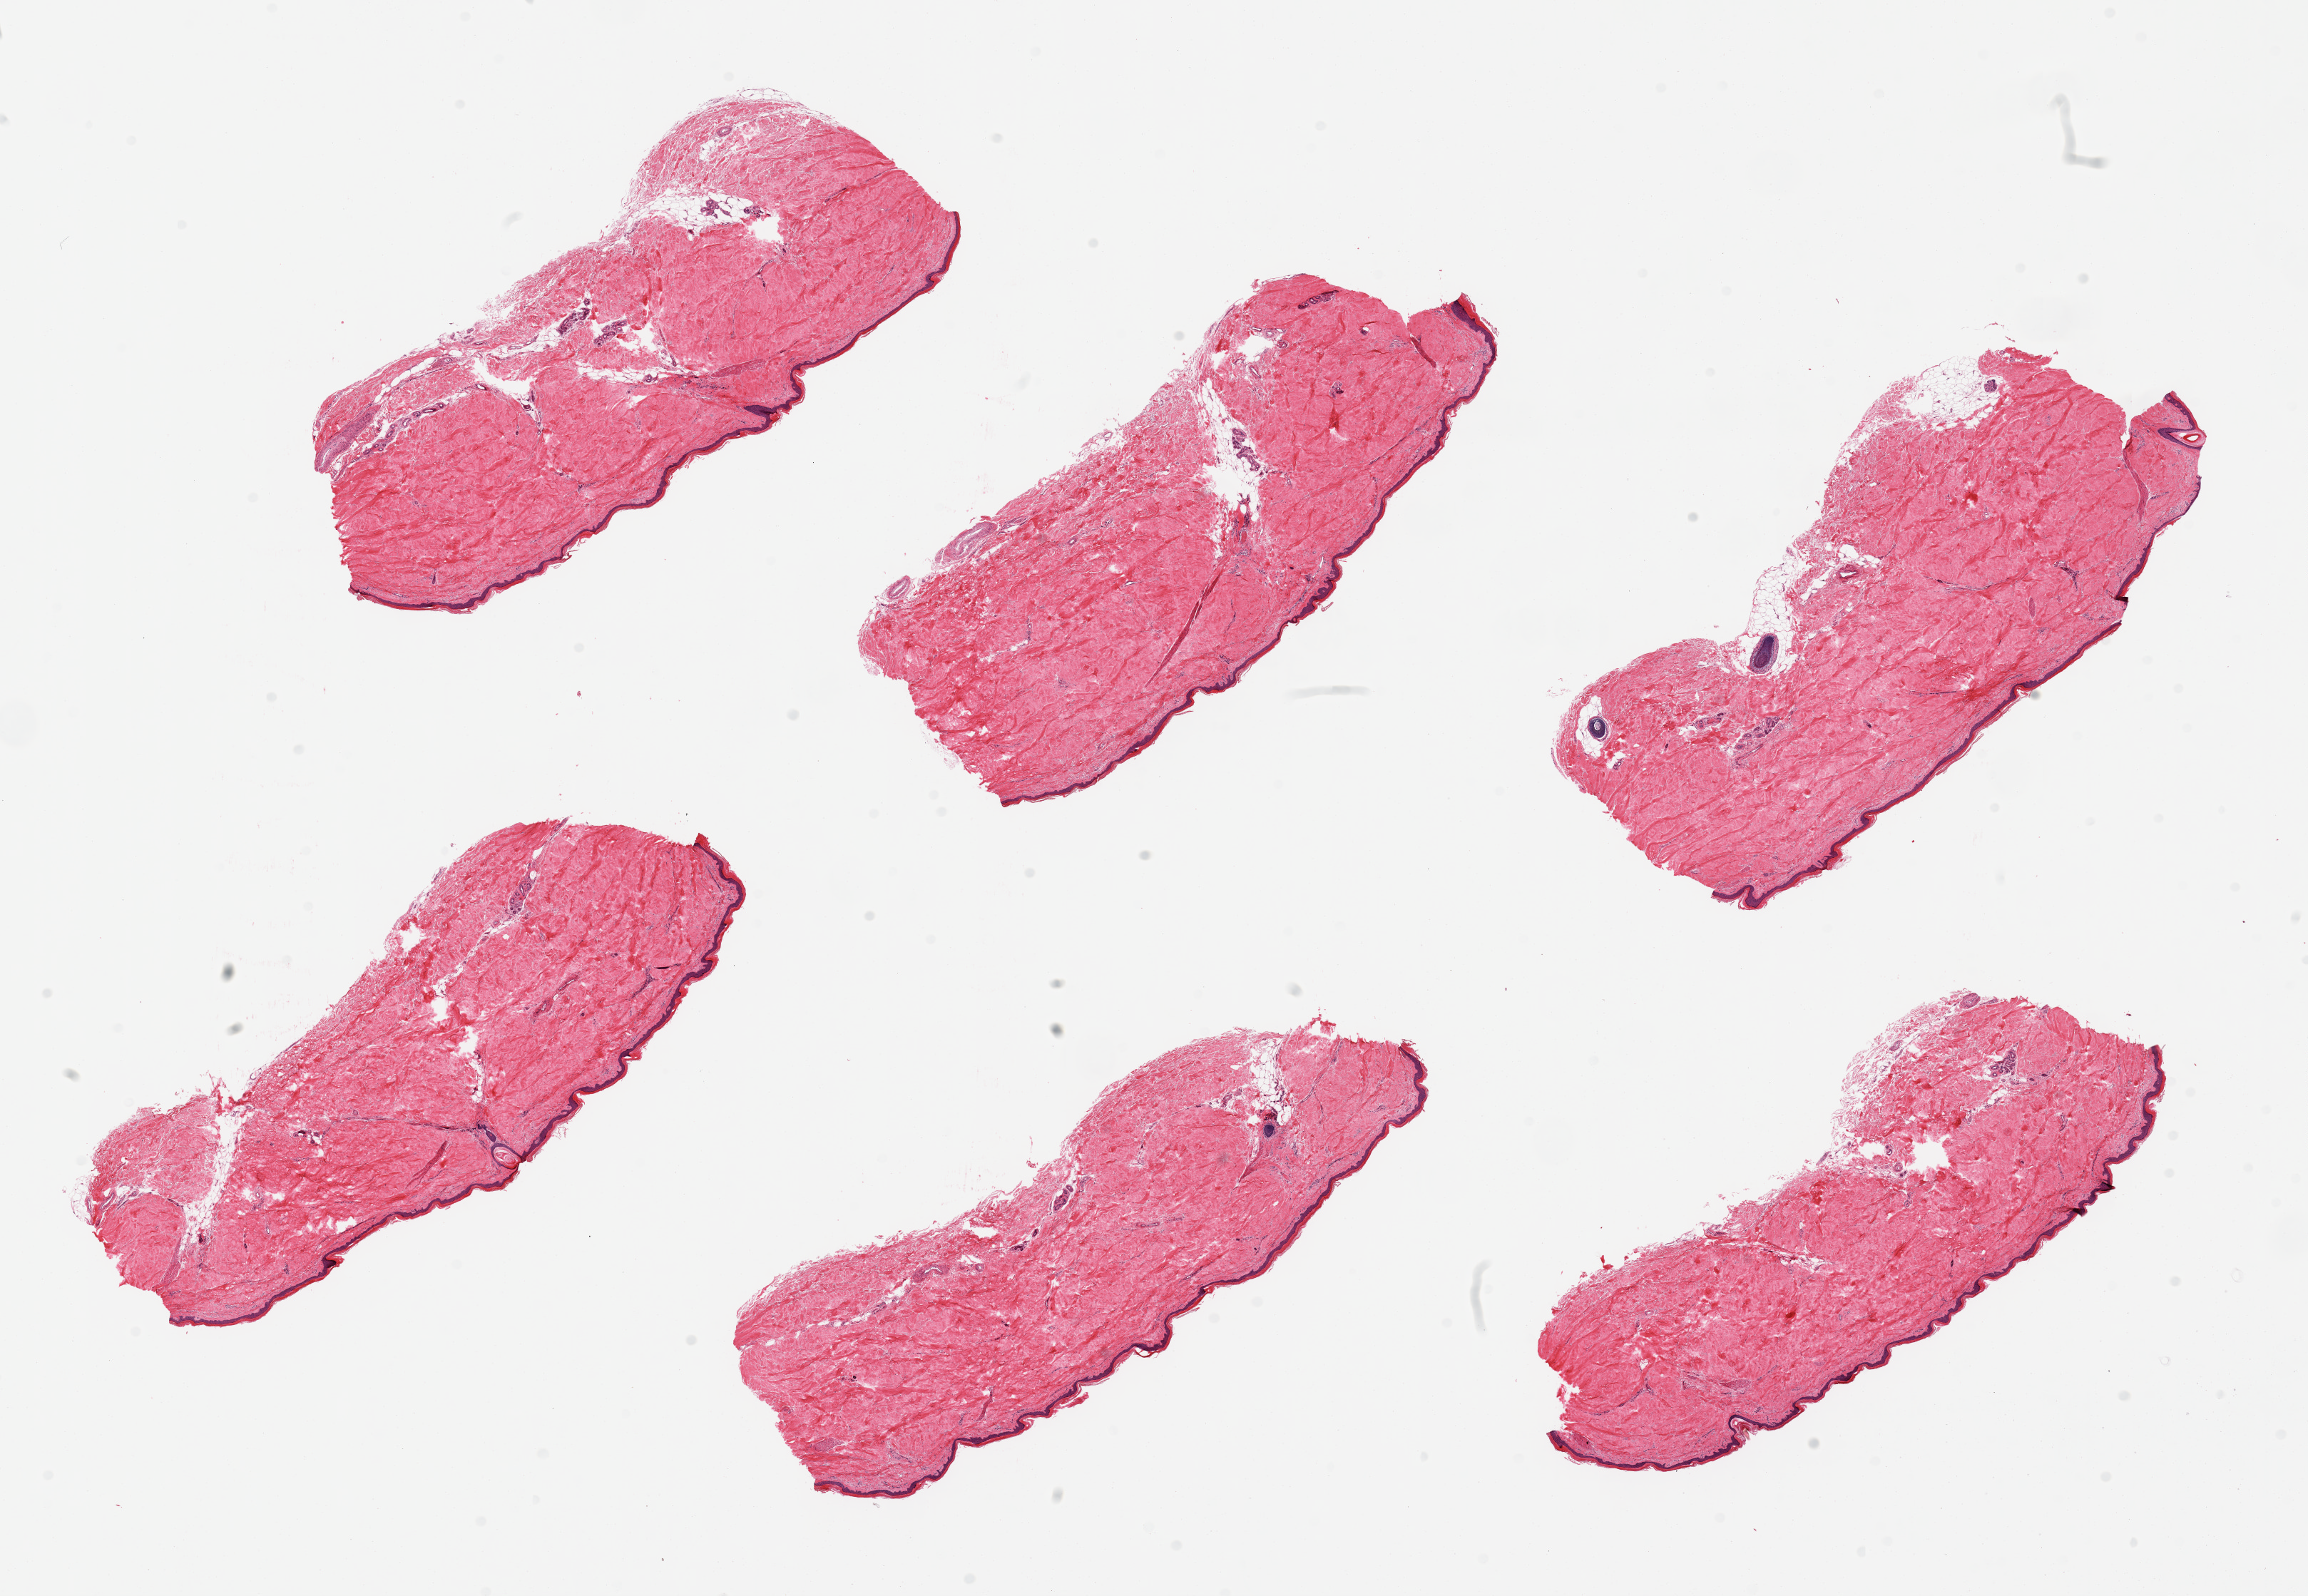
Whole-slide image, haematoxylin and eosin stain, brightfield, low-resolution overview of the scanned area, about 25.6 x 17.7 mm, PAXgene-fixed, paraffin-embedded tissue, target tissue: skin of lower leg, donor tissue sample. Male donor.
Pathologist's review note for this sample: 6 pieces; well trimmed; 5% intradermal fat.